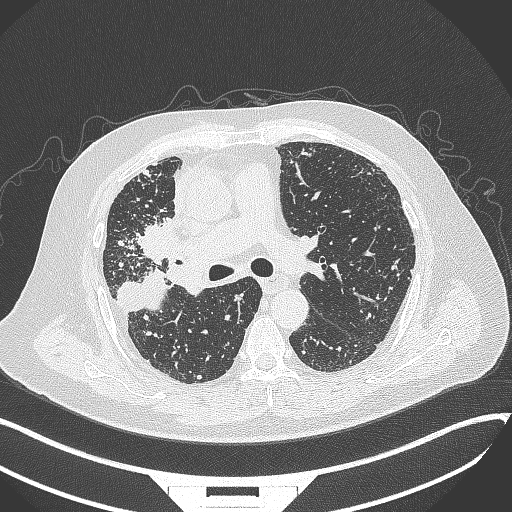
Chest CT, one axial slice. Position 210 of 384 along the scan axis. 120 kVp. Lung window (W 1500 / L -600 HU). 512 × 512 image matrix, field of view 400 × 400 mm. Patient: male, 69 years. Case-level facts recorded for this patient, not image findings: clinical TNM (as recorded): T4 N3 M1.
Annotated regions visible in this slice (rectangle marked by the reading radiologist):
- lung tumour (recorded histology: adenocarcinoma): bounding box <133,213,191,269> (left, top, right, bottom; pixels)